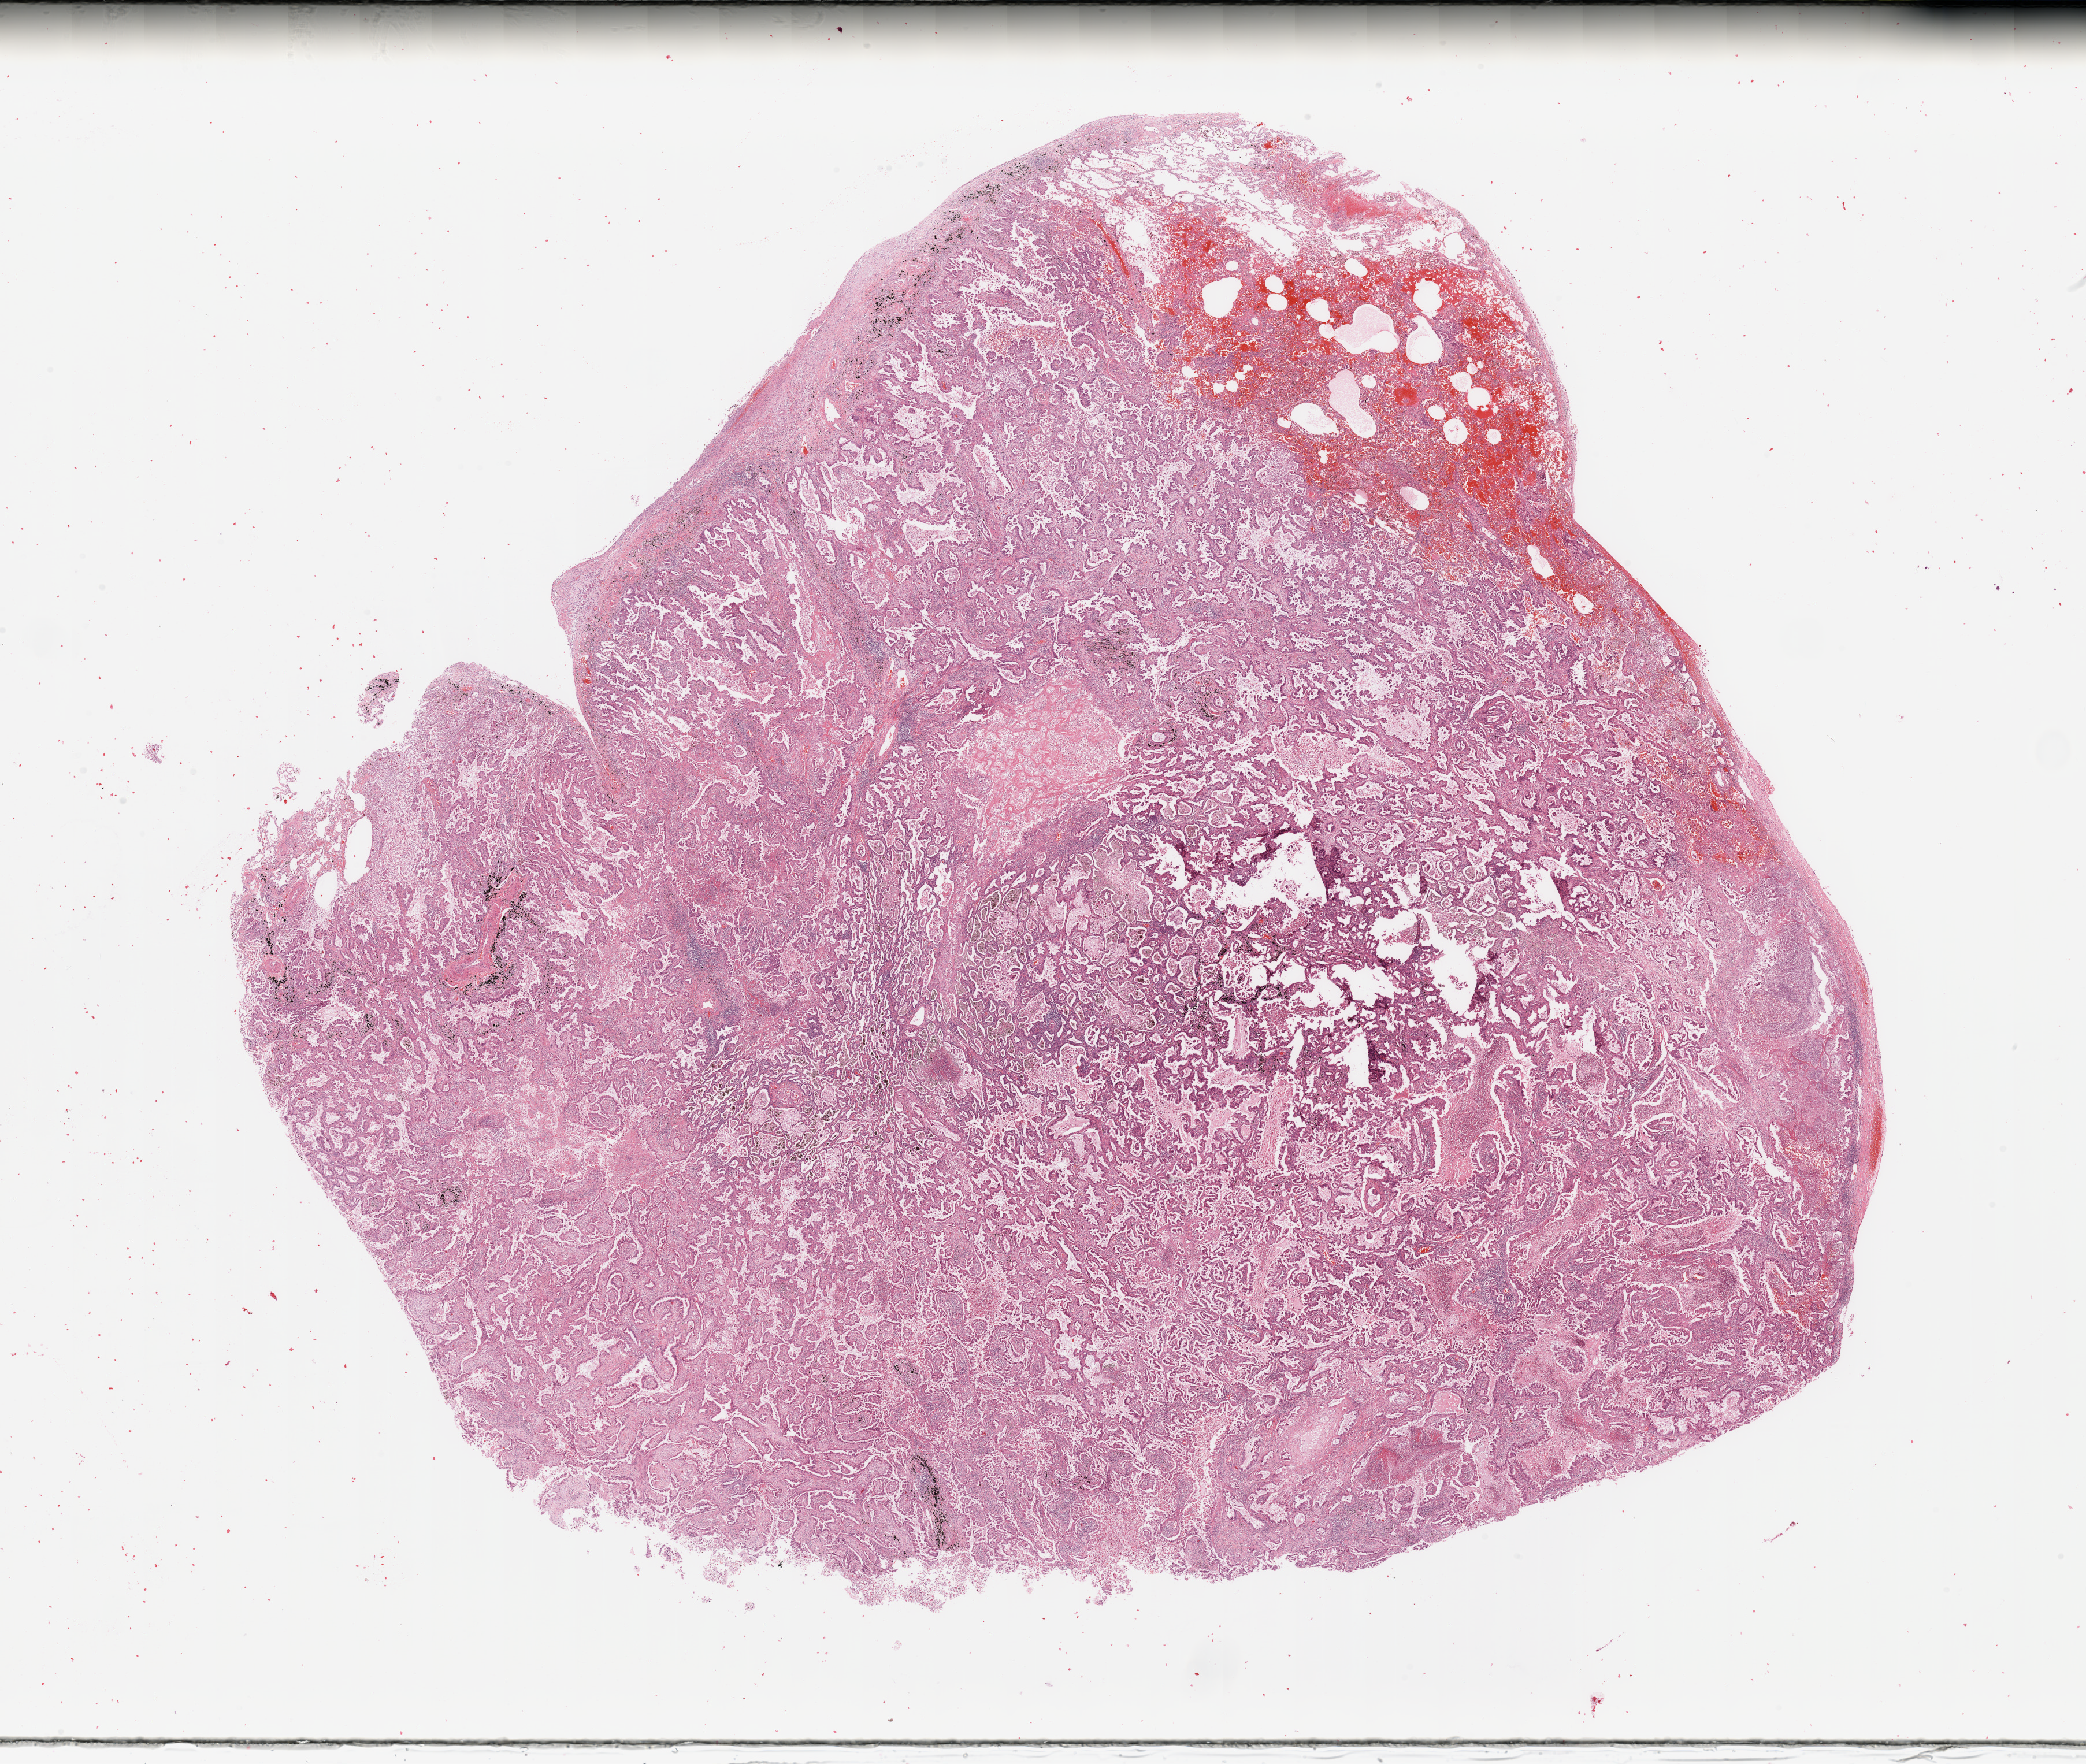
Digitized H&E-stained tissue section (whole slide), whole scanned area (about 28.5 x 24.1 mm, acquisition: 20x scan) shown as a low-resolution overview; tumour tissue sample, lung. Male, 58 y/o. Histologic grade: G2 (moderately differentiated).
Diagnosis: Adenocarcinoma, NOS. AJCC pathologic stage: IIIA.